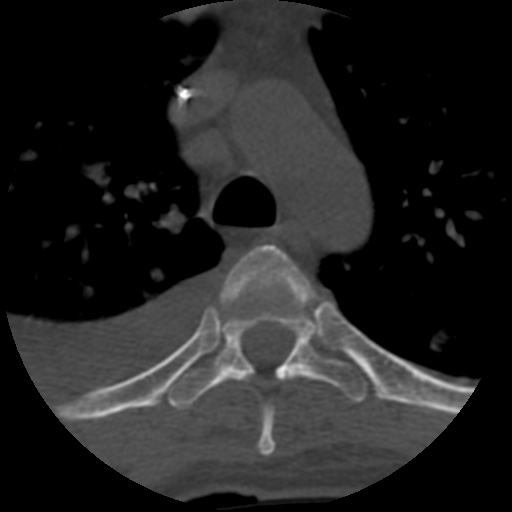
CT including the spine, one axial slice; position 461 of 708 along the scan axis; reconstruction kernel STANDARD; one of 3 acquisitions stored at this slice position; bone window (W 1800 / L 400 HU); 1.25 mm slice thickness; 512 × 512 image matrix, field of view 160 × 160 mm. Patient age 55 years. Case-level facts recorded for this patient, not image findings: primary cancer: colon.
Outlined on this slice (semi-automatic segmentation, software-assisted and operator-edited):
- T4 vertebra: bounding box <219,243,313,457> (left, top, right, bottom; pixels)
- T5 vertebra: <168,302,369,410>